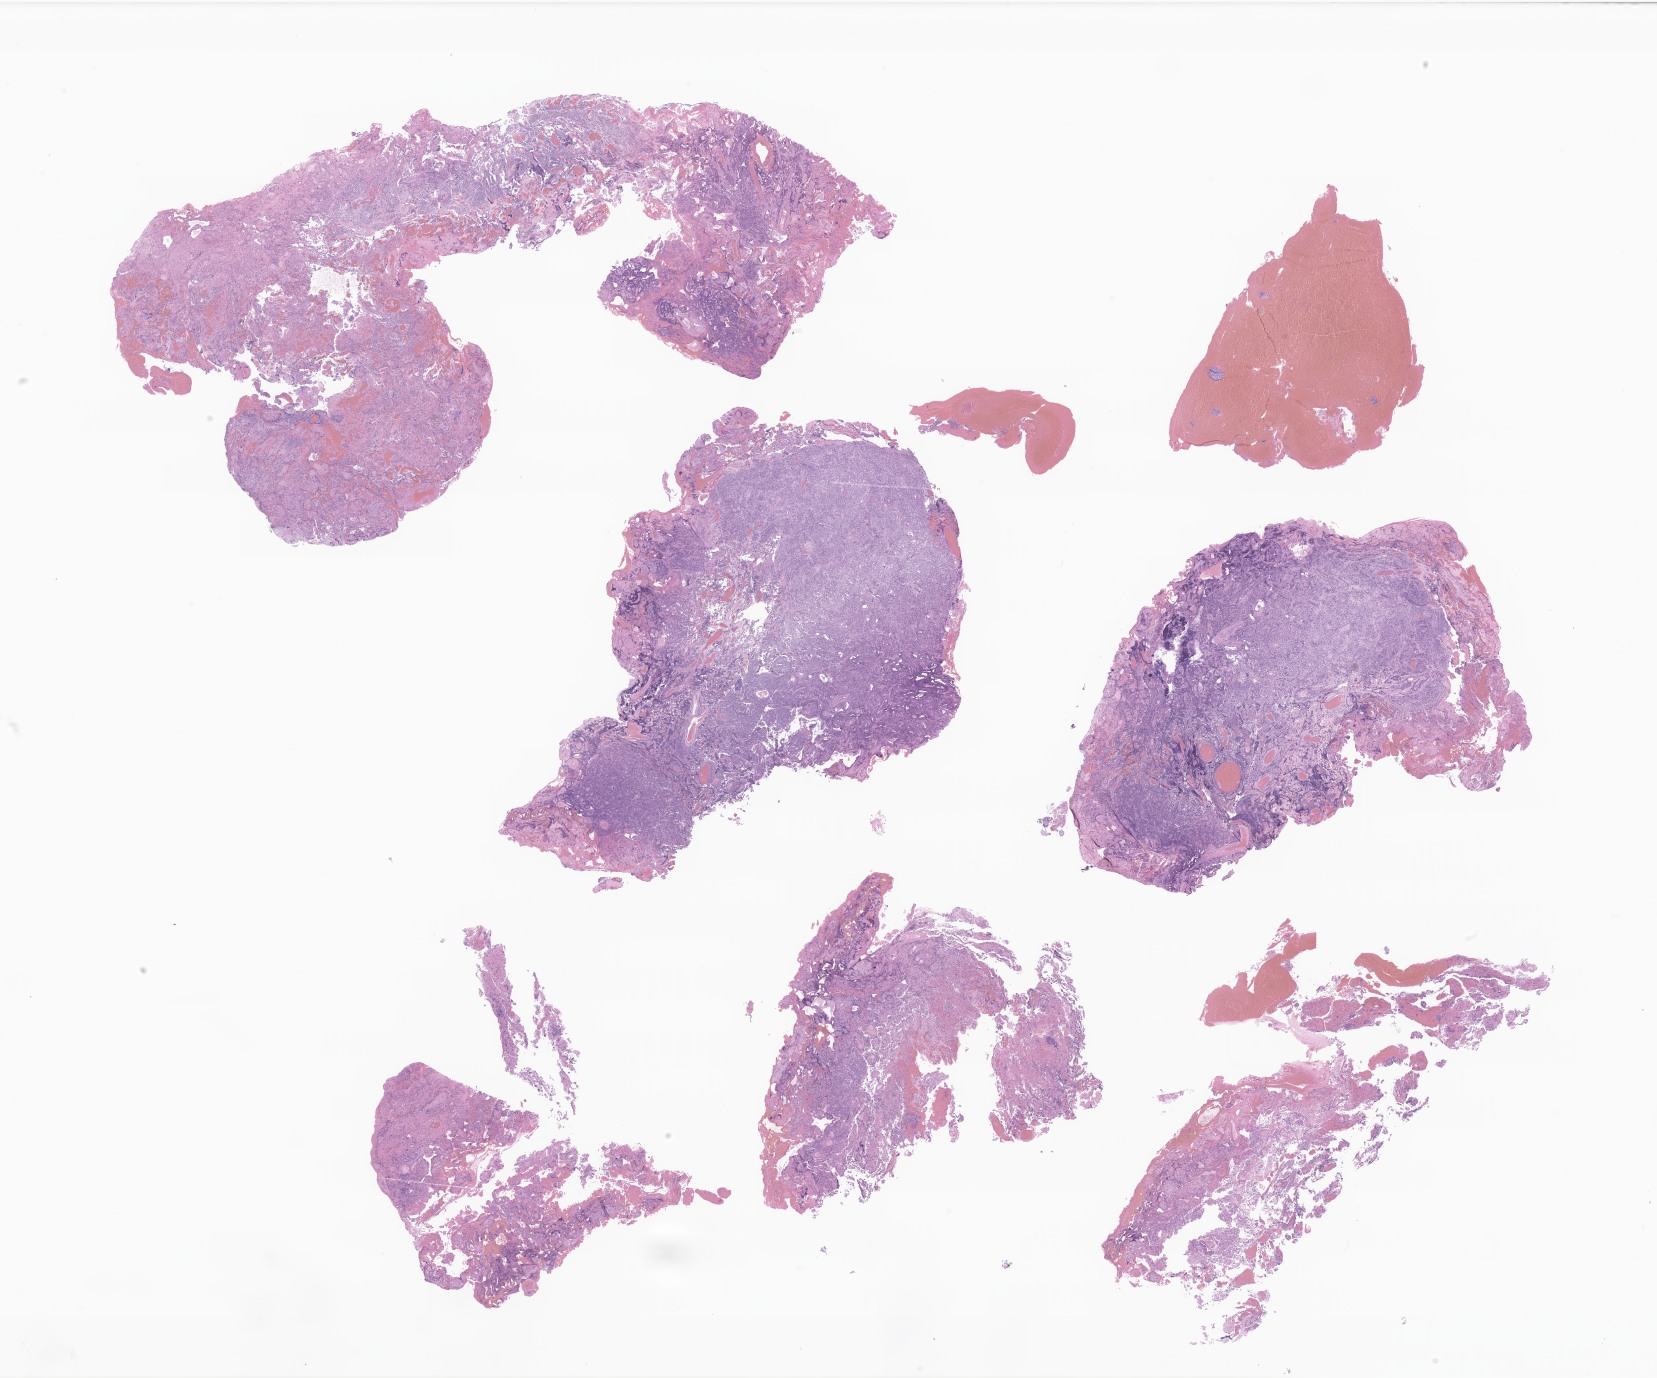
Haematoxylin and eosin whole-slide image of tumor tissue from the cerebellum — low-resolution overview of the scanned area, about 27.9 x 23.2 mm; formalin-fixed paraffin-embedded section. Male patient, age 83 months (6 years 11 months).
Recorded diagnosis: Medulloblastoma, NOS.